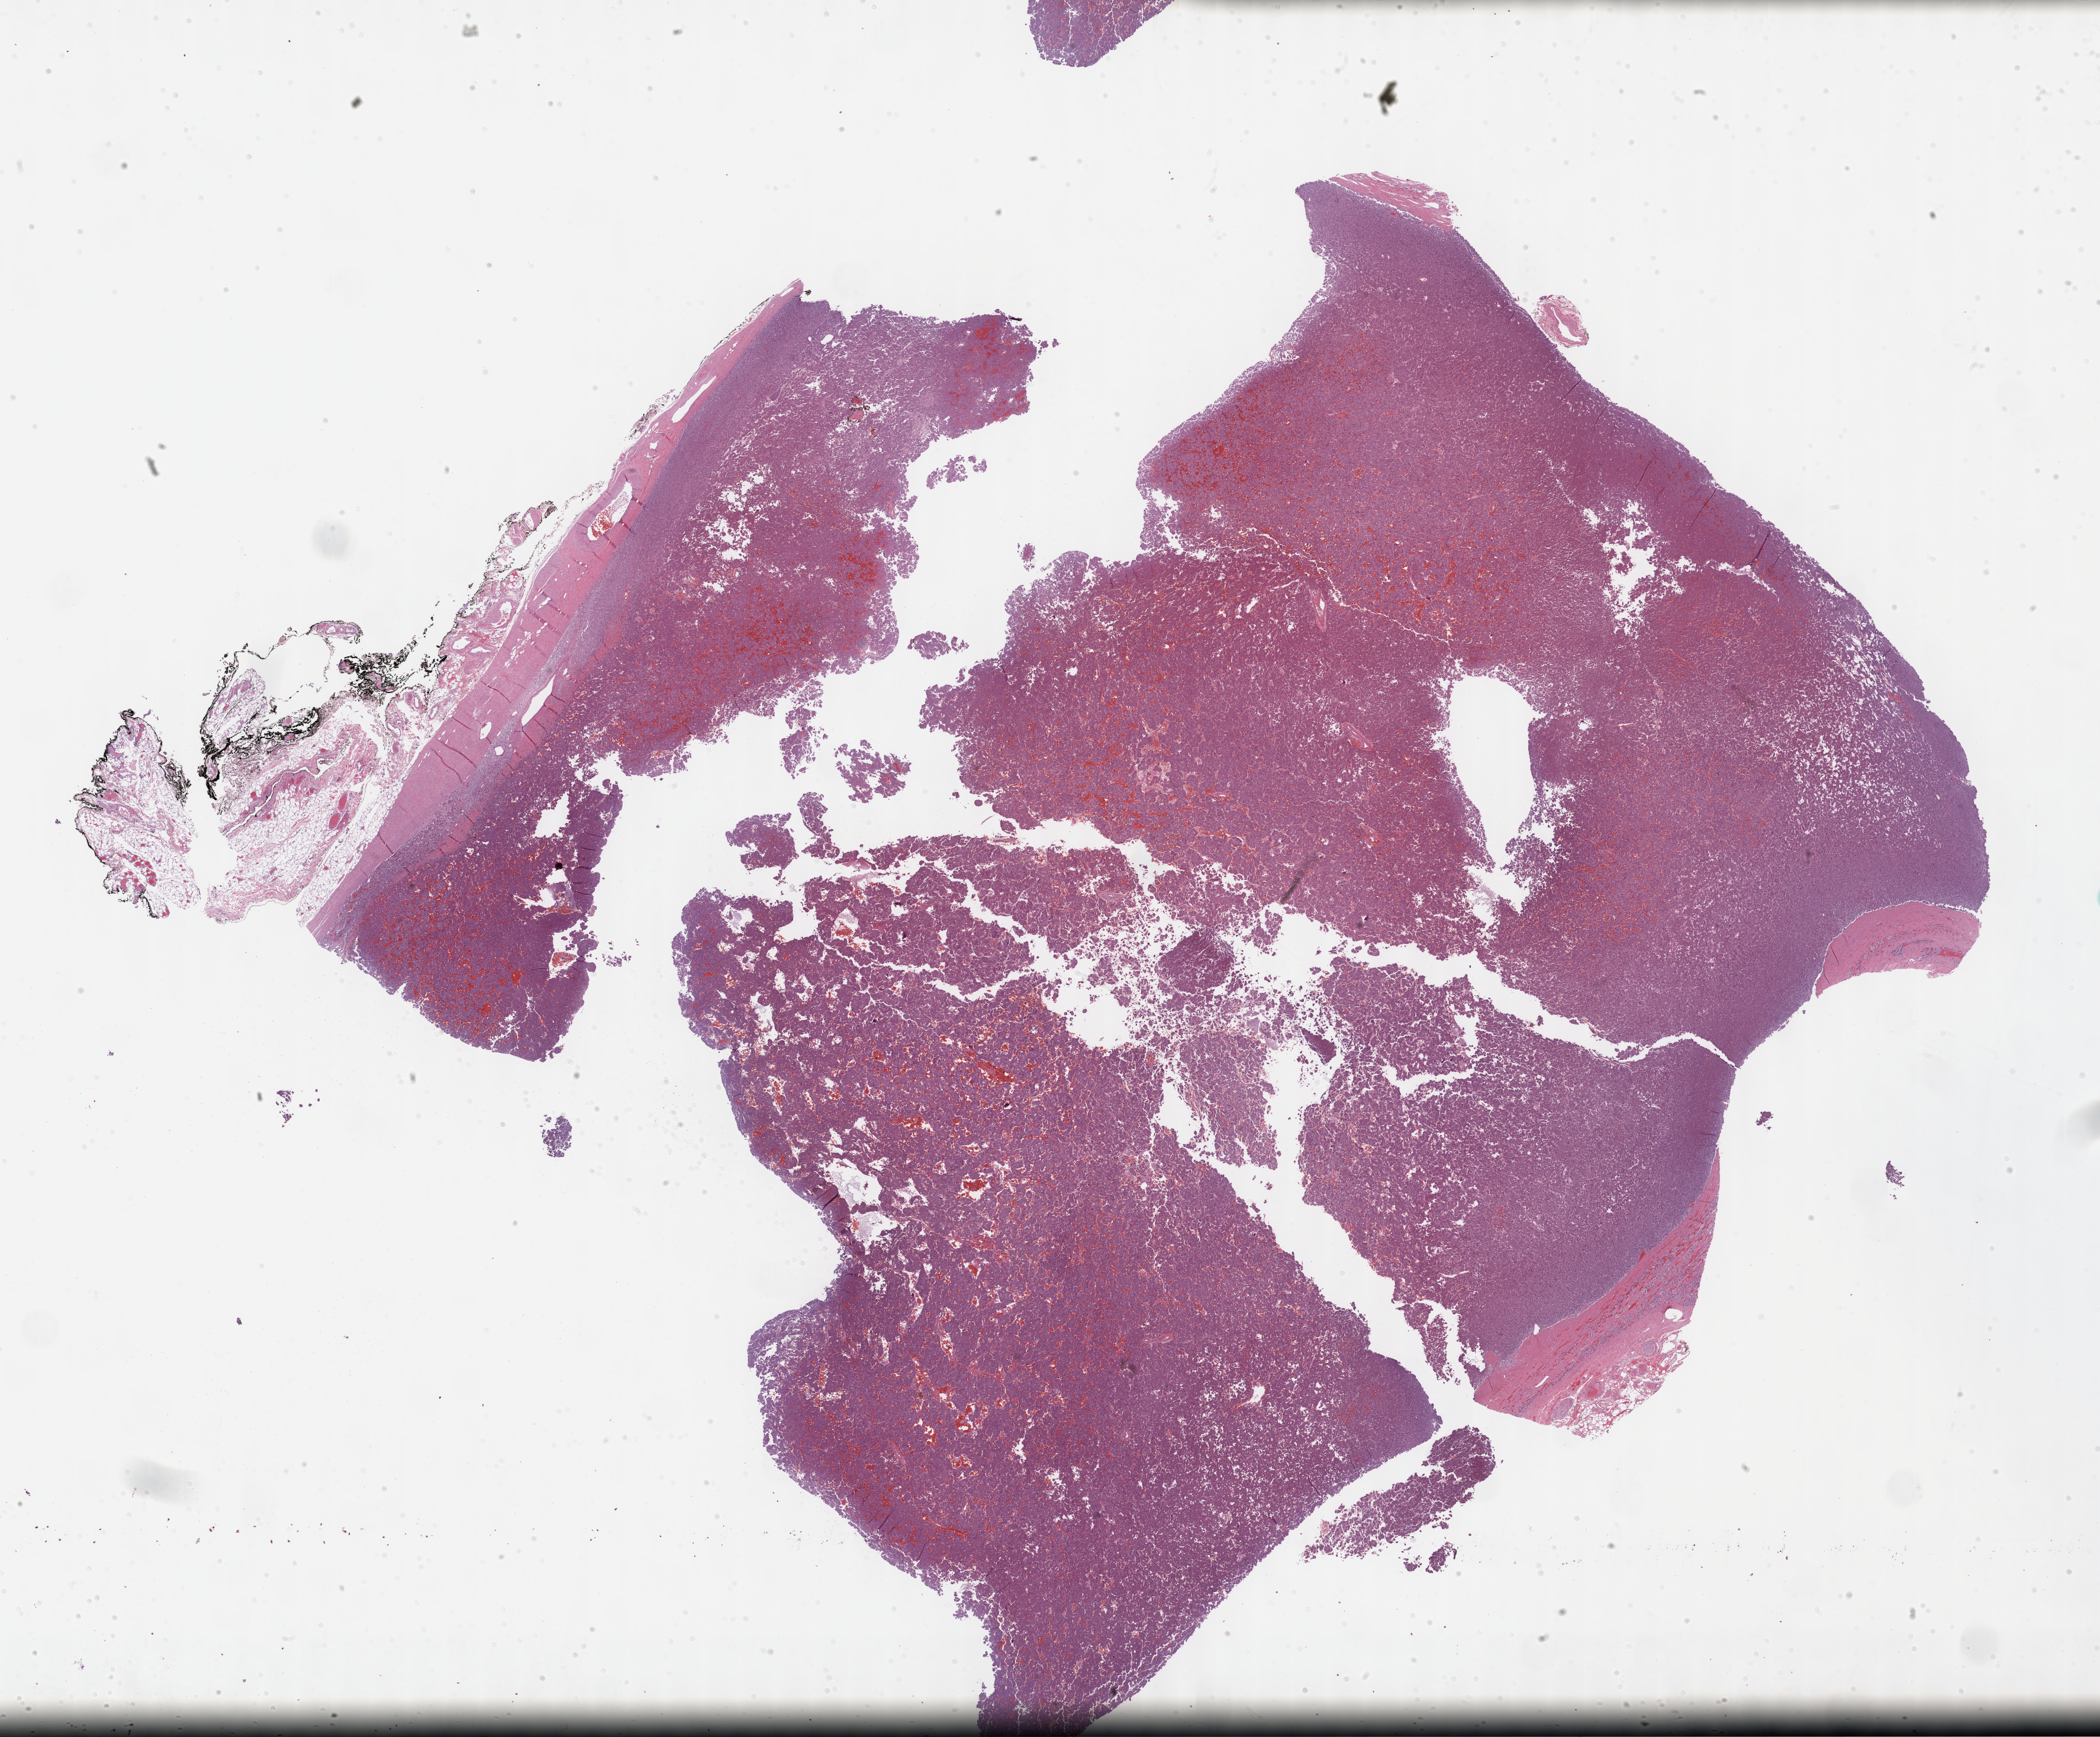
Digitized H&E-stained tissue section (whole slide), shown as a low-resolution overview of the whole scanned area (about 28.7 x 23.7 mm), FFPE section, adrenal gland, primary tumour sample. Patient: female, age at initial diagnosis 69 years.
• laterality: right
• histologic diagnosis: Pheochromocytoma, NOS